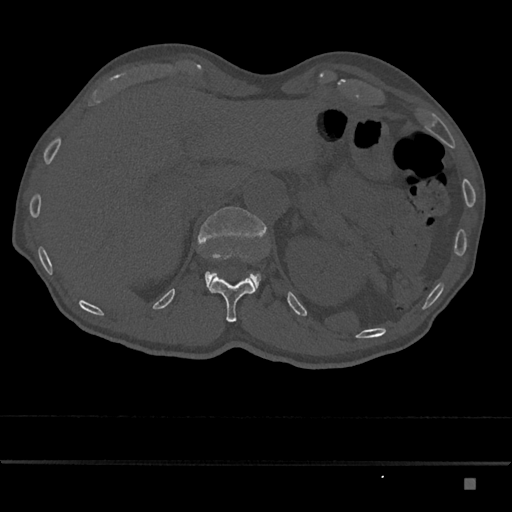
CT including the spine, one axial slice; position 588 of 797 along the scan axis; 120 kVp; bone window (W 1800 / L 400 HU); 512 × 512 image matrix, field of view 390 × 390 mm. Male patient, age 72 years. Case-level facts recorded for this patient, not image findings: primary cancer: prostate.
Annotated regions visible in this slice (semi-automatic segmentation, software-assisted and operator-edited):
- L1 vertebra: bounding box <197,207,267,292> (left, top, right, bottom; pixels)
- T12 vertebra: <208,276,255,322>